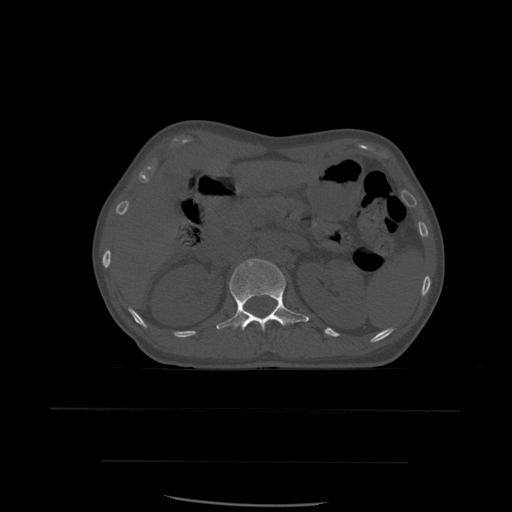
CT including the spine, one axial slice; position 250 of 574 along the scan axis; bone window (W 1800 / L 400 HU); 1.25 mm slice thickness; 512 × 512 image matrix, field of view 392 × 392 mm. Patient age 48 years. From the clinical record (not read from this slice): primary cancer: lung; vertebrae with lytic lesions (as recorded): T11.
Structures marked on this image (semi-automatically segmented with operator editing):
- L1 vertebra: bounding box <216,259,310,331> (left, top, right, bottom; pixels)